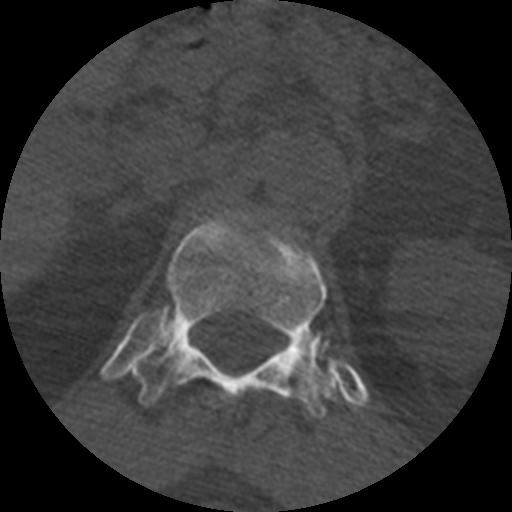
CT including the spine, one axial slice; position 385 of 399 along the scan axis; 120 kVp; bone window (W 1800 / L 400 HU); 1.25 mm slice thickness; 512 × 512 image matrix, field of view 160 × 160 mm. Patient age 71 years. From the clinical record (not read from this slice): primary cancer: prostate.
Structures marked on this image (semi-automatically segmented with operator editing):
- T12 vertebra: box from (x=133, y=218) to (x=337, y=418) px